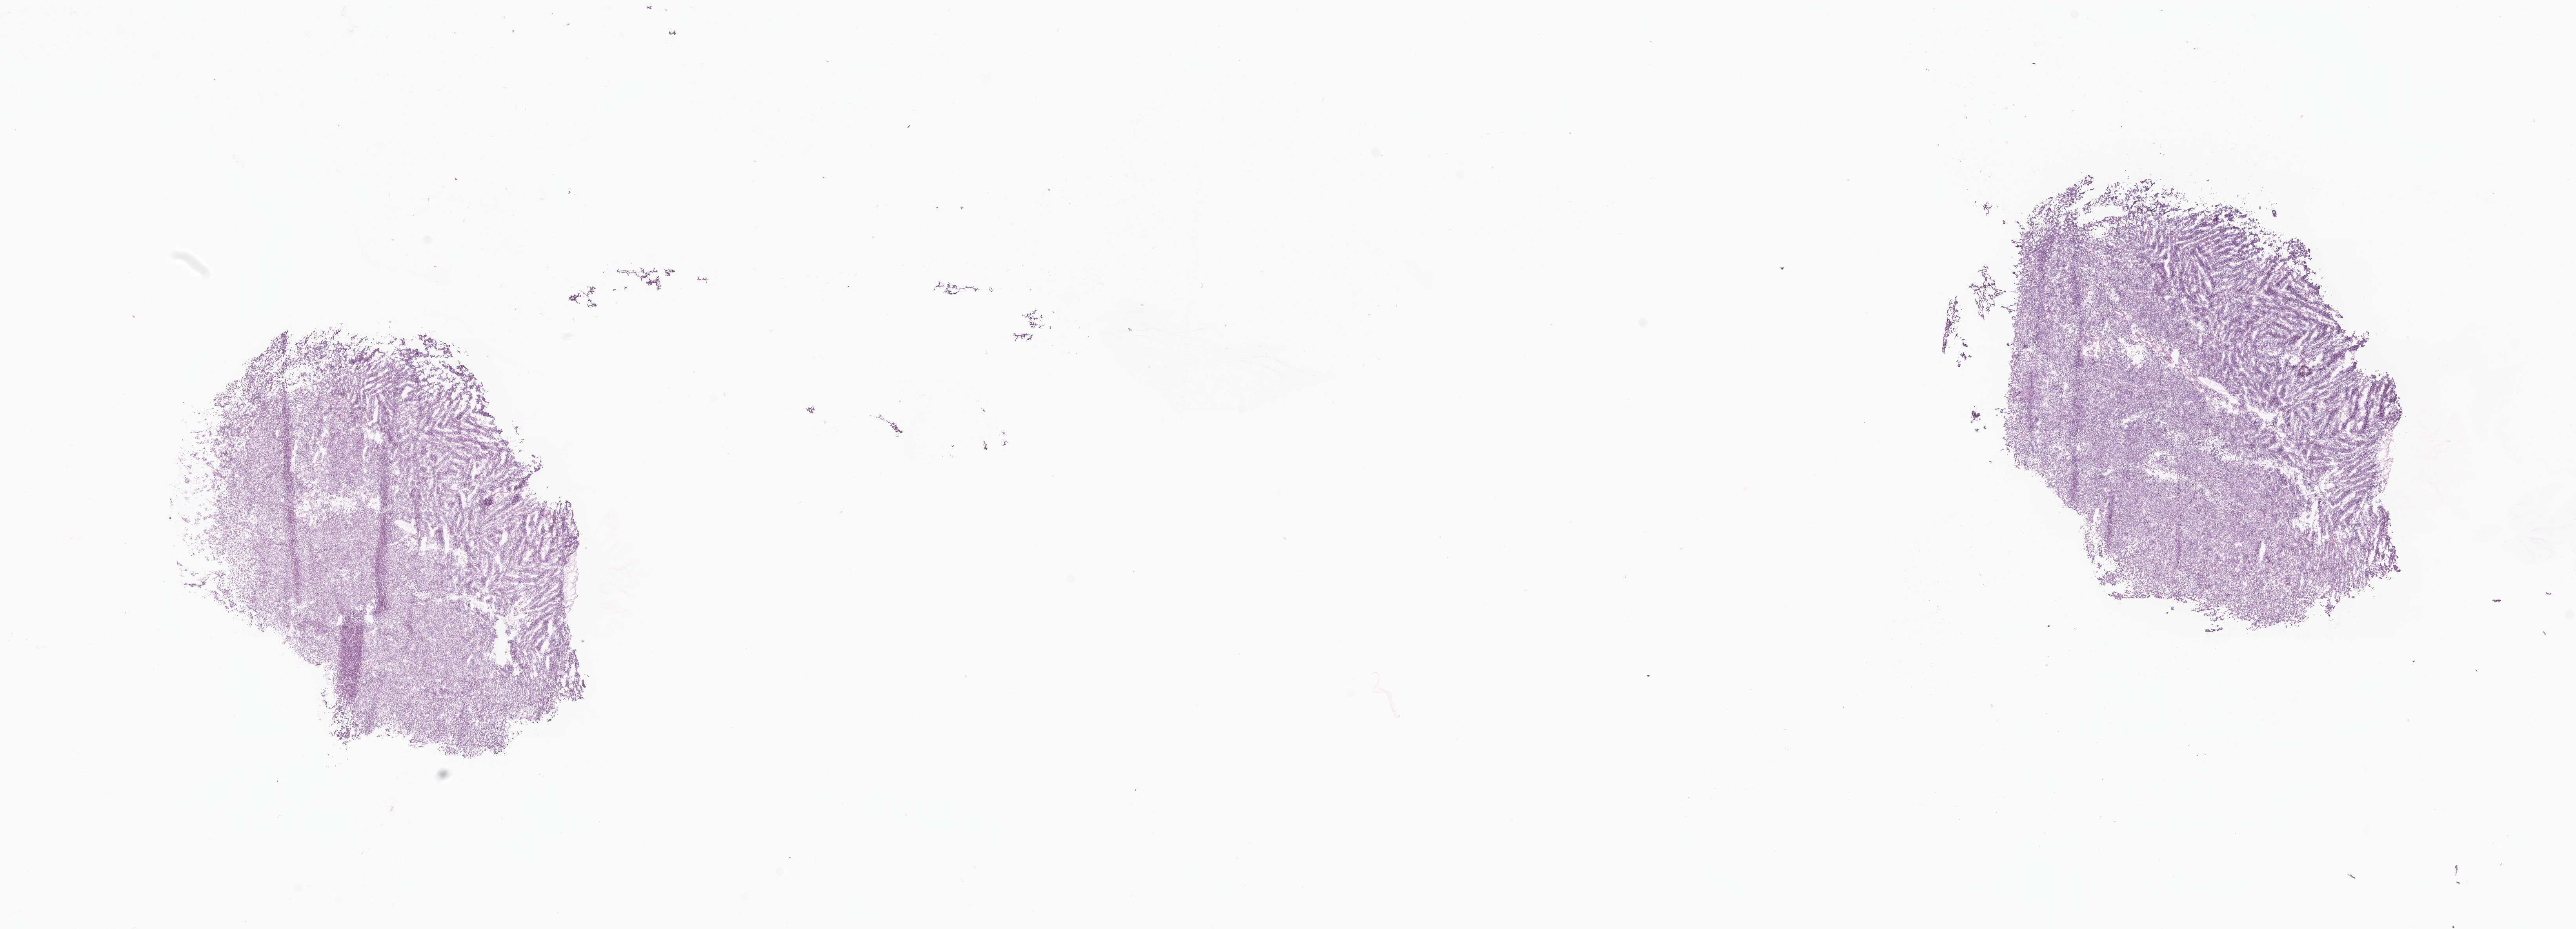
Digitized H&E-stained section of tumor tissue from the brain — shown as a low-resolution overview of the whole scanned area (about 27.7 x 10.0 mm); cryosection (OCT / tissue freezing medium). Male patient, age 206 months (17 years 2 months).
Recorded diagnosis: Medulloblastoma, NOS.